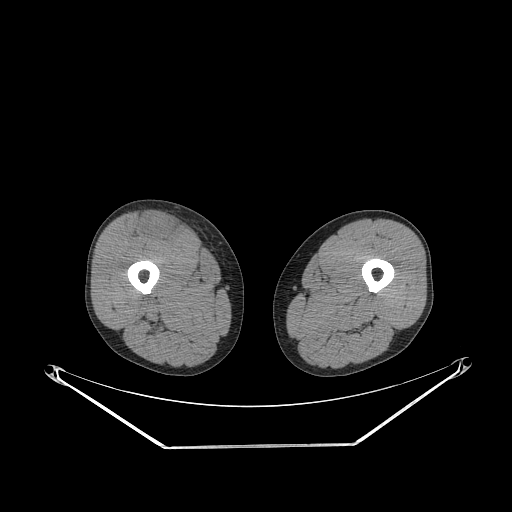
CT of an extremity soft-tissue mass (from a PET/CT study), one axial slice. Slice 252 of 311 in the series (ordered by position). Reconstruction kernel STANDARD. 140 kVp. Soft-tissue window (W 400 / L 40 HU). 3.75 mm slice thickness. 512 × 512 image matrix, field of view 500 × 500 mm. Male patient. Case-level facts recorded for this patient, not image findings: histological type: pleiomorphic leiomyosarcoma; grade: intermediate; site of the primary tumour: right thigh.
Structures marked on this image (expert contour drawn on MRI and transferred to this co-registered scan by the dataset authors):
- gross tumour volume including surrounding oedema: bounding box [x1, y1, x2, y2] px = [141, 214, 179, 243]